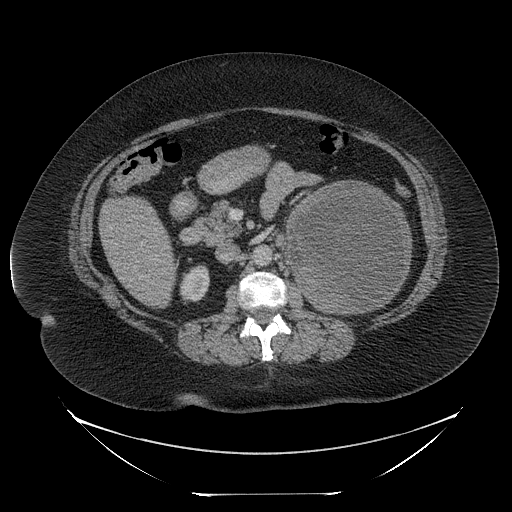
Contrast-enhanced abdominal CT, one axial slice; position 129 of 205 along the scan axis; reconstruction kernel STANDARD; 120 kVp; intravenous contrast given; soft-tissue window (W 400 / L 40 HU); 2.5 mm slice thickness; 512 × 512 image matrix. Patient: female, 53 years. Case-level facts recorded for this patient, not image findings: diagnosis: adrenocortical carcinoma; tumour side: left adrenal; tumour size at pathology: 17 cm.
Annotated regions visible in this slice (semi-automatic segmentation, software-assisted and operator-edited):
- mass: bounding box [x1, y1, x2, y2] px = [289, 183, 411, 313]